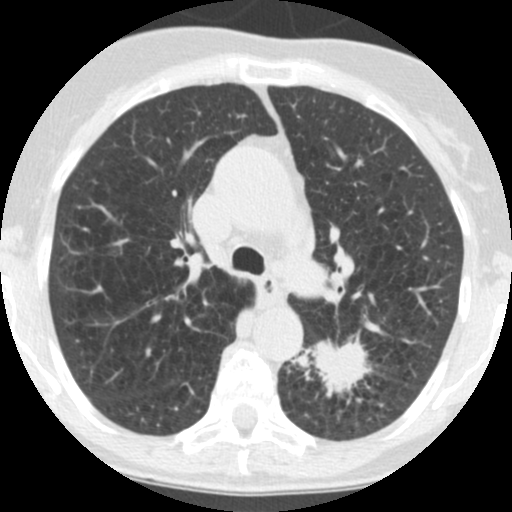
Chest CT (low-dose screening protocol), one axial image. Third screening round (two years after baseline). Lung window (W 1500 / L -600 HU). 2.5 mm slice thickness. Standard (soft-tissue) reconstruction kernel (STANDARD). Female, age 71 years at enrolment. Current smoker at enrolment.
Expert reader's lesion annotation, bounding box [x1, y1, x2, y2] px = [298, 331, 380, 411]. The screening reader recorded 2 non-calcified nodules or masses ≥4 mm on this exam (left lower lobe, left lower lobe); which of them this box marks is not recorded.